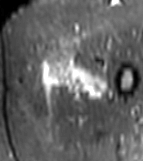
MRI of an extremity soft-tissue mass, one axial slice. Position 15 of 81 along the scan axis. STIR. MR volume resampled by the dataset authors to the PET/CT grid (not the native acquisition matrix). 143 × 161 image matrix. Female patient. From the clinical record (not read from this slice): histological type: myxofibrosarcoma; grade: intermediate; site of the primary tumour: left thigh.
Annotated regions visible in this slice (expert contour drawn on MRI and transferred to this co-registered scan by the dataset authors):
- gross tumour volume including surrounding oedema: bounding box <37,56,112,102> (left, top, right, bottom; pixels)
- gross tumour volume (mass): <53,56,98,82>